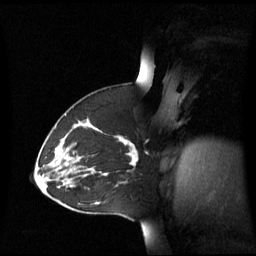
Breast MRI (dynamic contrast-enhanced), one sagittal slice. Position 38 of 60 along the scan axis. Dynamic contrast-enhanced series, image 2 of 3 at this slice position (ordered by acquisition). 1.5 T. TE 4.2 ms, TR 8.4 ms. 256 × 256 image matrix, field of view 270 × 270 mm. Female patient, age 43 years. Case-level facts recorded for this patient, not image findings: setting: breast cancer imaged before/during neoadjuvant chemotherapy; receptor status: triple-negative.
Annotated regions visible in this slice (semi-automatically segmented with operator editing):
- analysis volume of interest (the breast-tissue region the enhancement analysis was run in; not a lesion): box from (x=55, y=124) to (x=138, y=173) px
- tumour enhancement mask (voxels above the 70 % enhancement threshold inside the analysis volume of interest): (x=77, y=137)–(x=138, y=173)